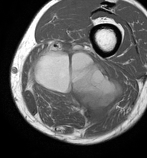
MRI of an extremity soft-tissue mass, one axial slice; MR volume resampled by the dataset authors to the PET/CT grid (not the native acquisition matrix); 3.27 mm slice thickness; 147 × 158 image matrix, field of view 144 × 154 mm. Male patient. From the clinical record (not read from this slice): histological type: undifferentiated pleomorphic liposarcoma; grade: high; site of the primary tumour: left thigh.
Annotated regions visible in this slice (expert contour drawn on MRI and transferred to this co-registered scan by the dataset authors):
- gross tumour volume including surrounding oedema: box from (x=28, y=40) to (x=122, y=127) px
- gross tumour volume (mass): (x=32, y=51)–(x=118, y=121)